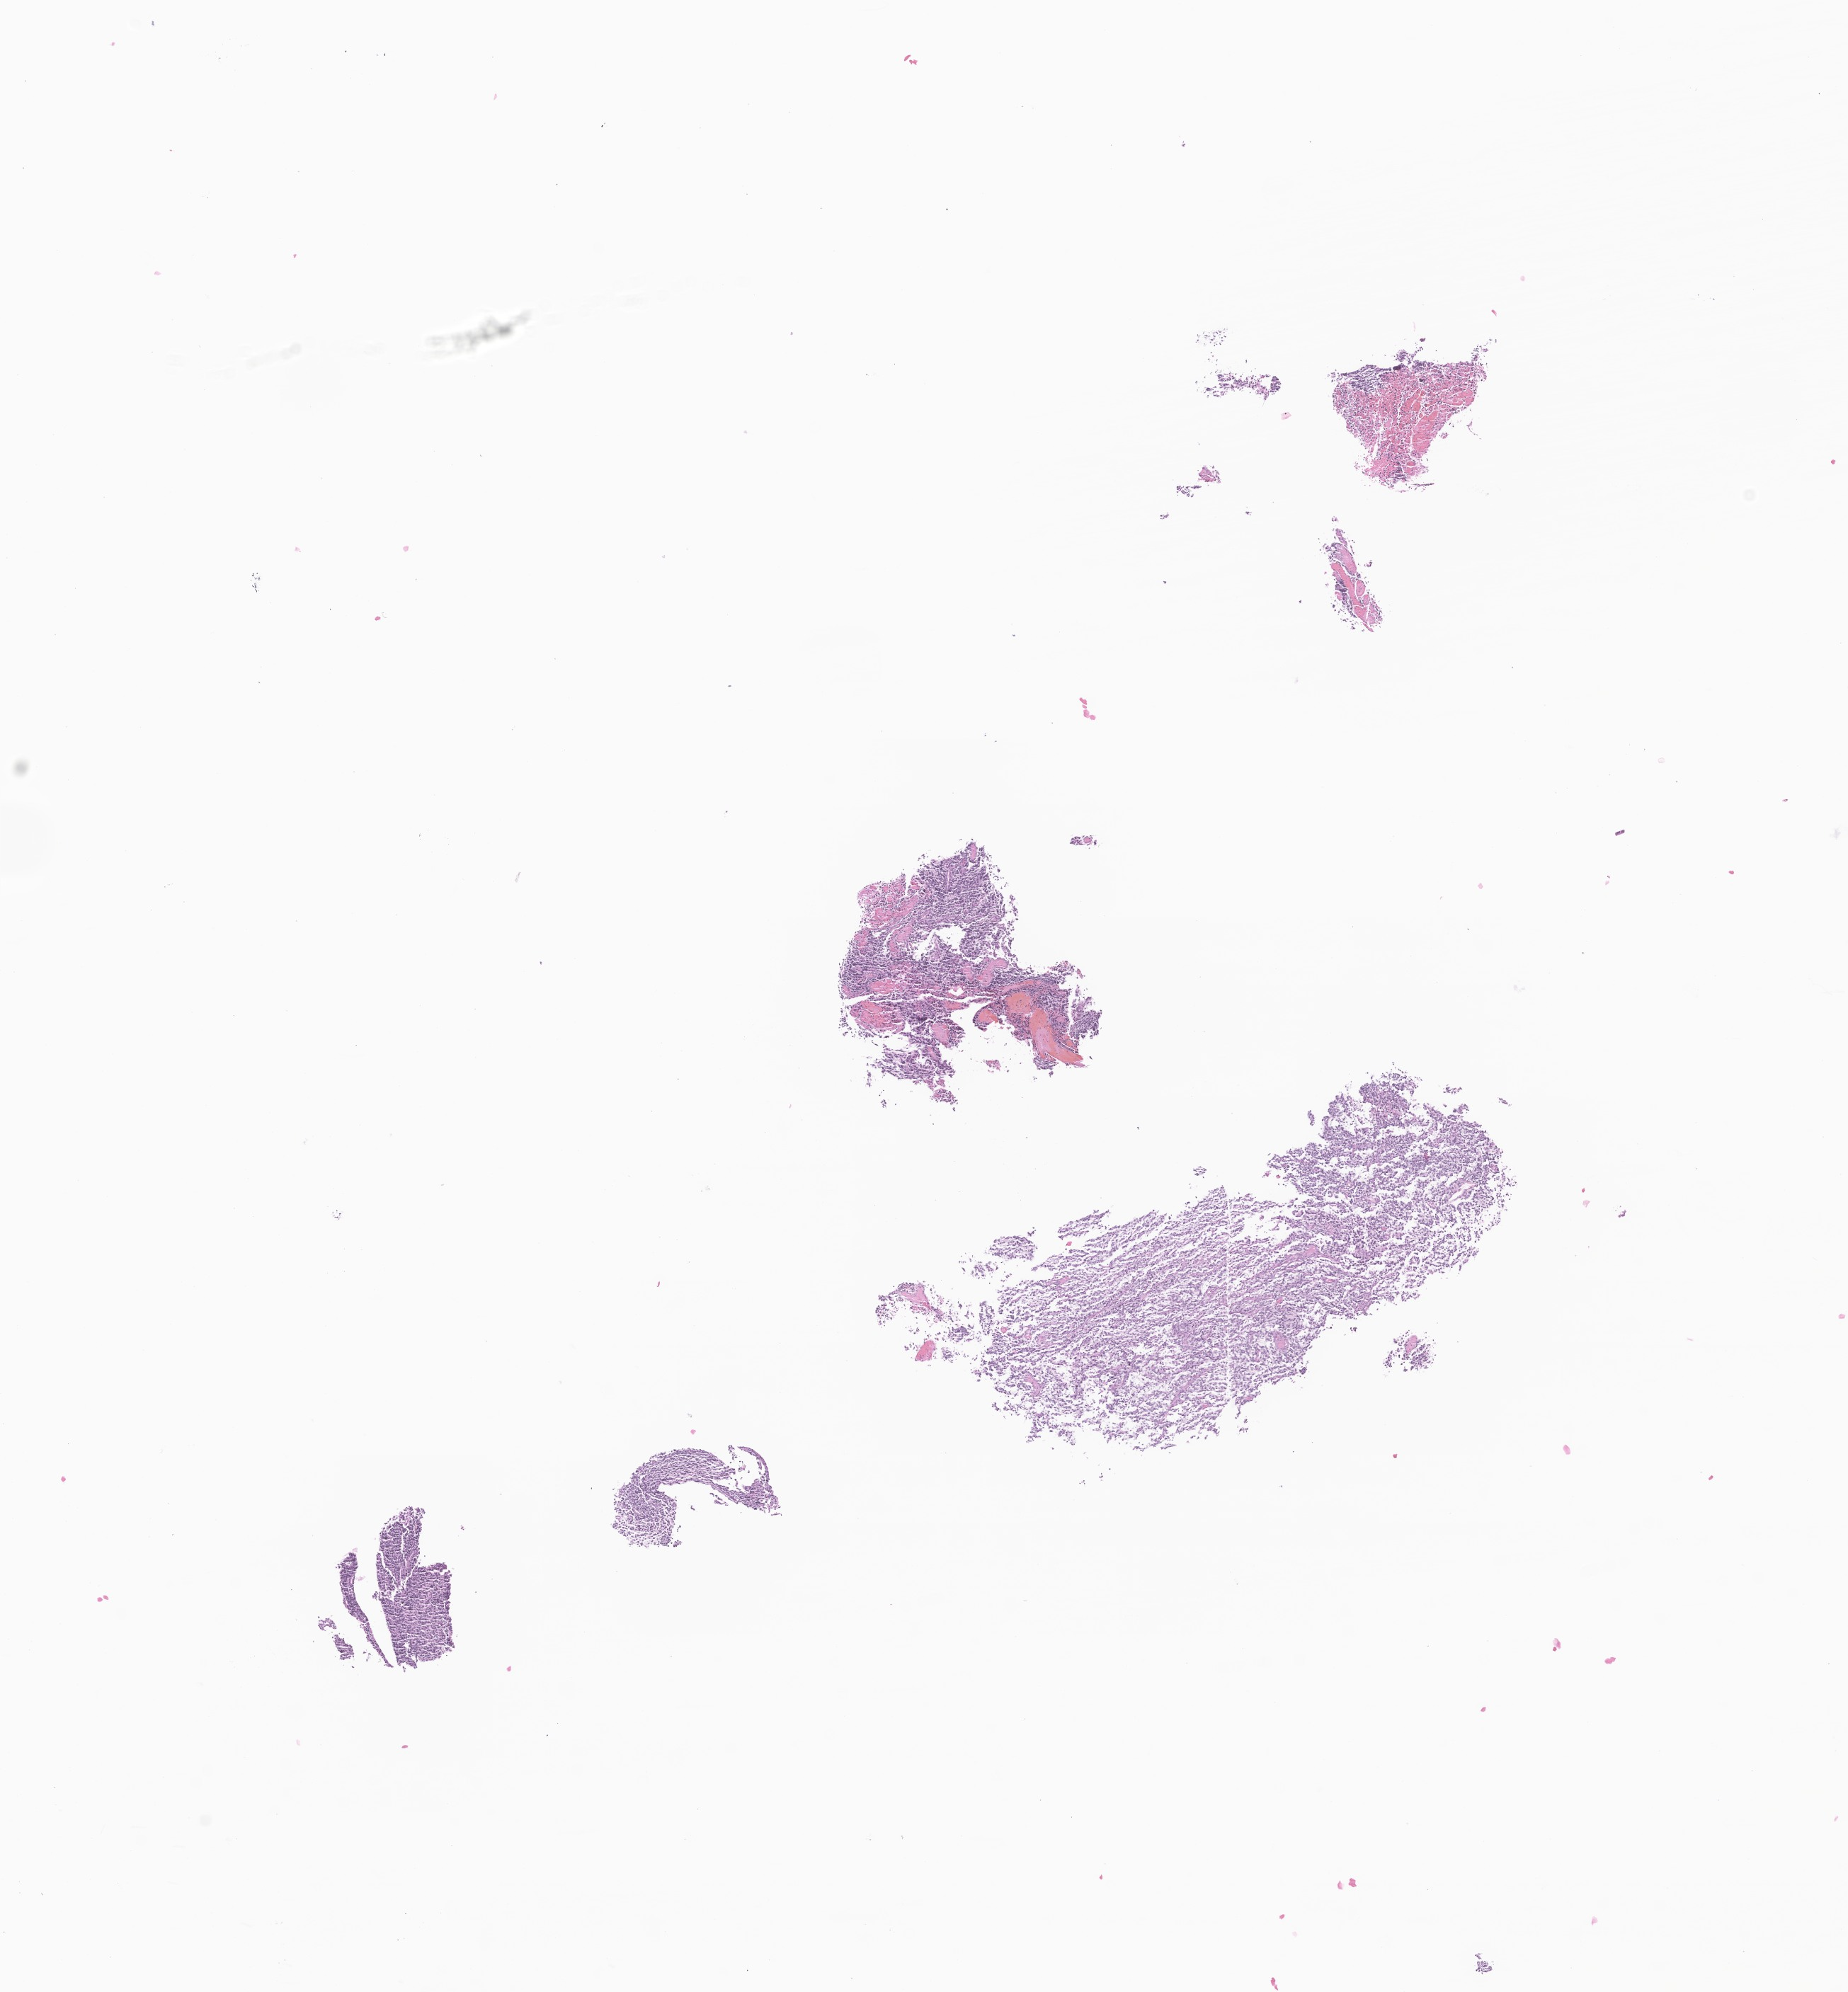
H&E whole-slide image of tumor tissue from the parietal lobe — low-resolution overview of the scanned area, about 11.0 x 11.9 mm; formalin-fixed, paraffin-embedded (FFPE) tissue. Female patient, age 638 days (about 1.7 years).
- diagnosis (ICD-O-3 morphology term): Embryonal carcinoma, NOS